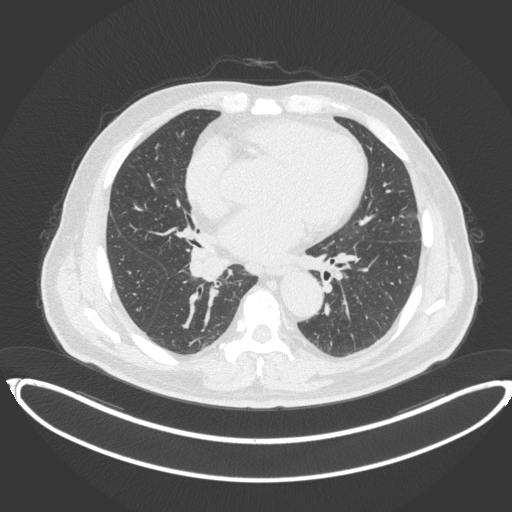
Chest CT, one axial slice; position 193 of 383 along the scan axis; 120 kVp; lung window (W 1500 / L -600 HU); 1 mm slice thickness; 512 × 512 image matrix, field of view 448 × 448 mm. Patient: male, 61 years. From the clinical record (not read from this slice): clinical TNM (as recorded): T1b N1 M0.
Outlined on this slice (bounding box drawn by a radiologist):
- lung tumour (recorded histology: squamous cell carcinoma): box from (x=189, y=242) to (x=228, y=286) px